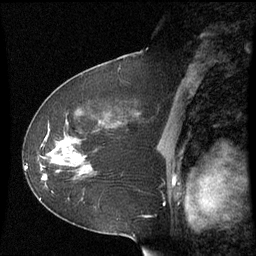
Breast MRI (dynamic contrast-enhanced), one sagittal slice. Slice 34 of 60 in the series (ordered by position). Dynamic contrast-enhanced series, image 2 of 3 at this slice position (ordered by acquisition). 1.5 T. TE 4.2 ms, TR 8.9 ms. 2.3 mm slice thickness. 256 × 256 image matrix, field of view 210 × 210 mm. Female patient, age 51 years. Case-level facts recorded for this patient, not image findings: setting: breast cancer imaged before/during neoadjuvant chemotherapy; receptor status: HR-positive, HER2-negative.
Outlined on this slice (semi-automatic segmentation, software-assisted and operator-edited):
- analysis volume of interest (the breast-tissue region the enhancement analysis was run in; not a lesion): box from (x=50, y=117) to (x=117, y=179) px
- tumour enhancement mask (voxels above the 70 % enhancement threshold inside the analysis volume of interest): (x=64, y=140)–(x=81, y=163)